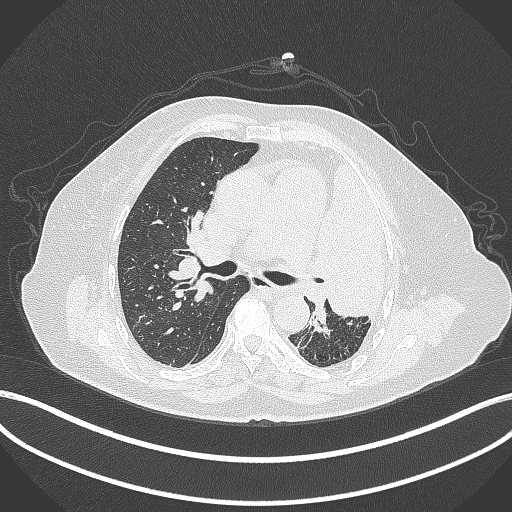
Chest CT, one axial slice; position 237 of 399 along the scan axis; reconstruction kernel B70f; 120 kVp; lung window (W 1500 / L -600 HU); 1 mm slice thickness; 512 × 512 image matrix, field of view 400 × 400 mm. Female patient, age 75 years. Case-level facts recorded for this patient, not image findings: clinical TNM (as recorded): T3 N3 M1.
Annotated regions visible in this slice (bounding box drawn by a radiologist):
- lung tumour (recorded histology: adenocarcinoma): bounding box [x1, y1, x2, y2] px = [315, 165, 394, 319]